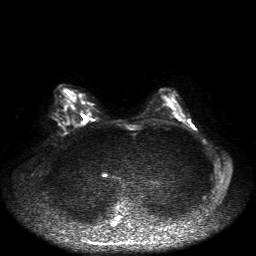
Breast MRI, one axial slice; slice 27 of 50 in the series (ordered by position); diffusion-weighted series; image 2 of 4 stored at this slice position (different b-values; order by instance number); 1.5 T; 4 mm slice thickness; 256 × 256 image matrix, field of view 360 × 360 mm. Female patient.
Structures marked on this image (expert manual segmentation):
- tumour on diffusion-weighted imaging: bounding box <81,115,88,124> (left, top, right, bottom; pixels)